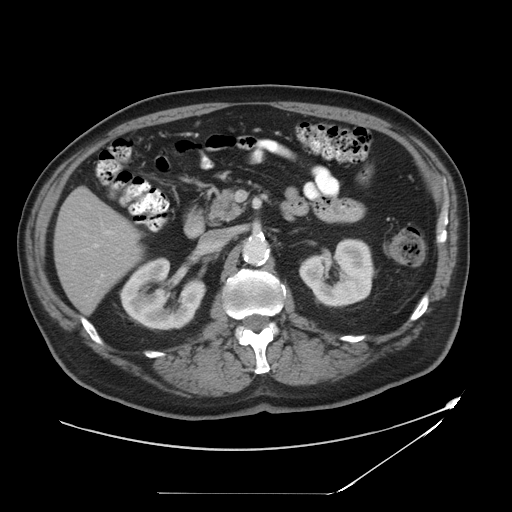
Contrast-enhanced abdominal CT, one axial slice. Position 20 of 49 along the scan axis. Intravenous contrast given. Soft-tissue window (W 400 / L 40 HU). 5 mm slice thickness. 512 × 512 image matrix, field of view 461 × 461 mm. Male patient, age 72 years. From the clinical record (not read from this slice): diagnosis: colorectal cancer liver metastases, imaged before liver resection; multiple liver metastases: no; largest metastasis: 2.5 cm; disease in both lobes: no.
Outlined on this slice (manually delineated by an expert):
- hepatic veins: bounding box [x1, y1, x2, y2] px = [81, 233, 103, 252]
- liver: [56, 190, 142, 313]
- planned liver remnant (the part of the liver to remain after resection): [56, 190, 142, 313]
- portal vein (with intrahepatic branches): [101, 230, 114, 278]